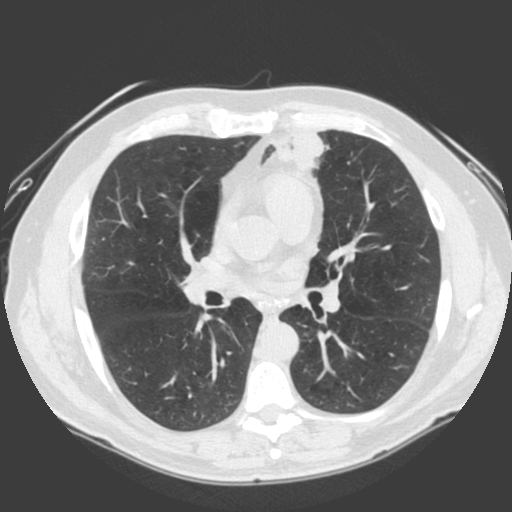
Low-dose screening chest CT, one axial slice. 120 kVp. Lung window (W 1500 / L -600 HU). 2 mm slice thickness. 512 × 512 image matrix.
Outlined on this slice (manually delineated by an expert):
- lesion 1 (tumor, lower lobe of left lung): box from (x=277, y=133) to (x=329, y=169) px